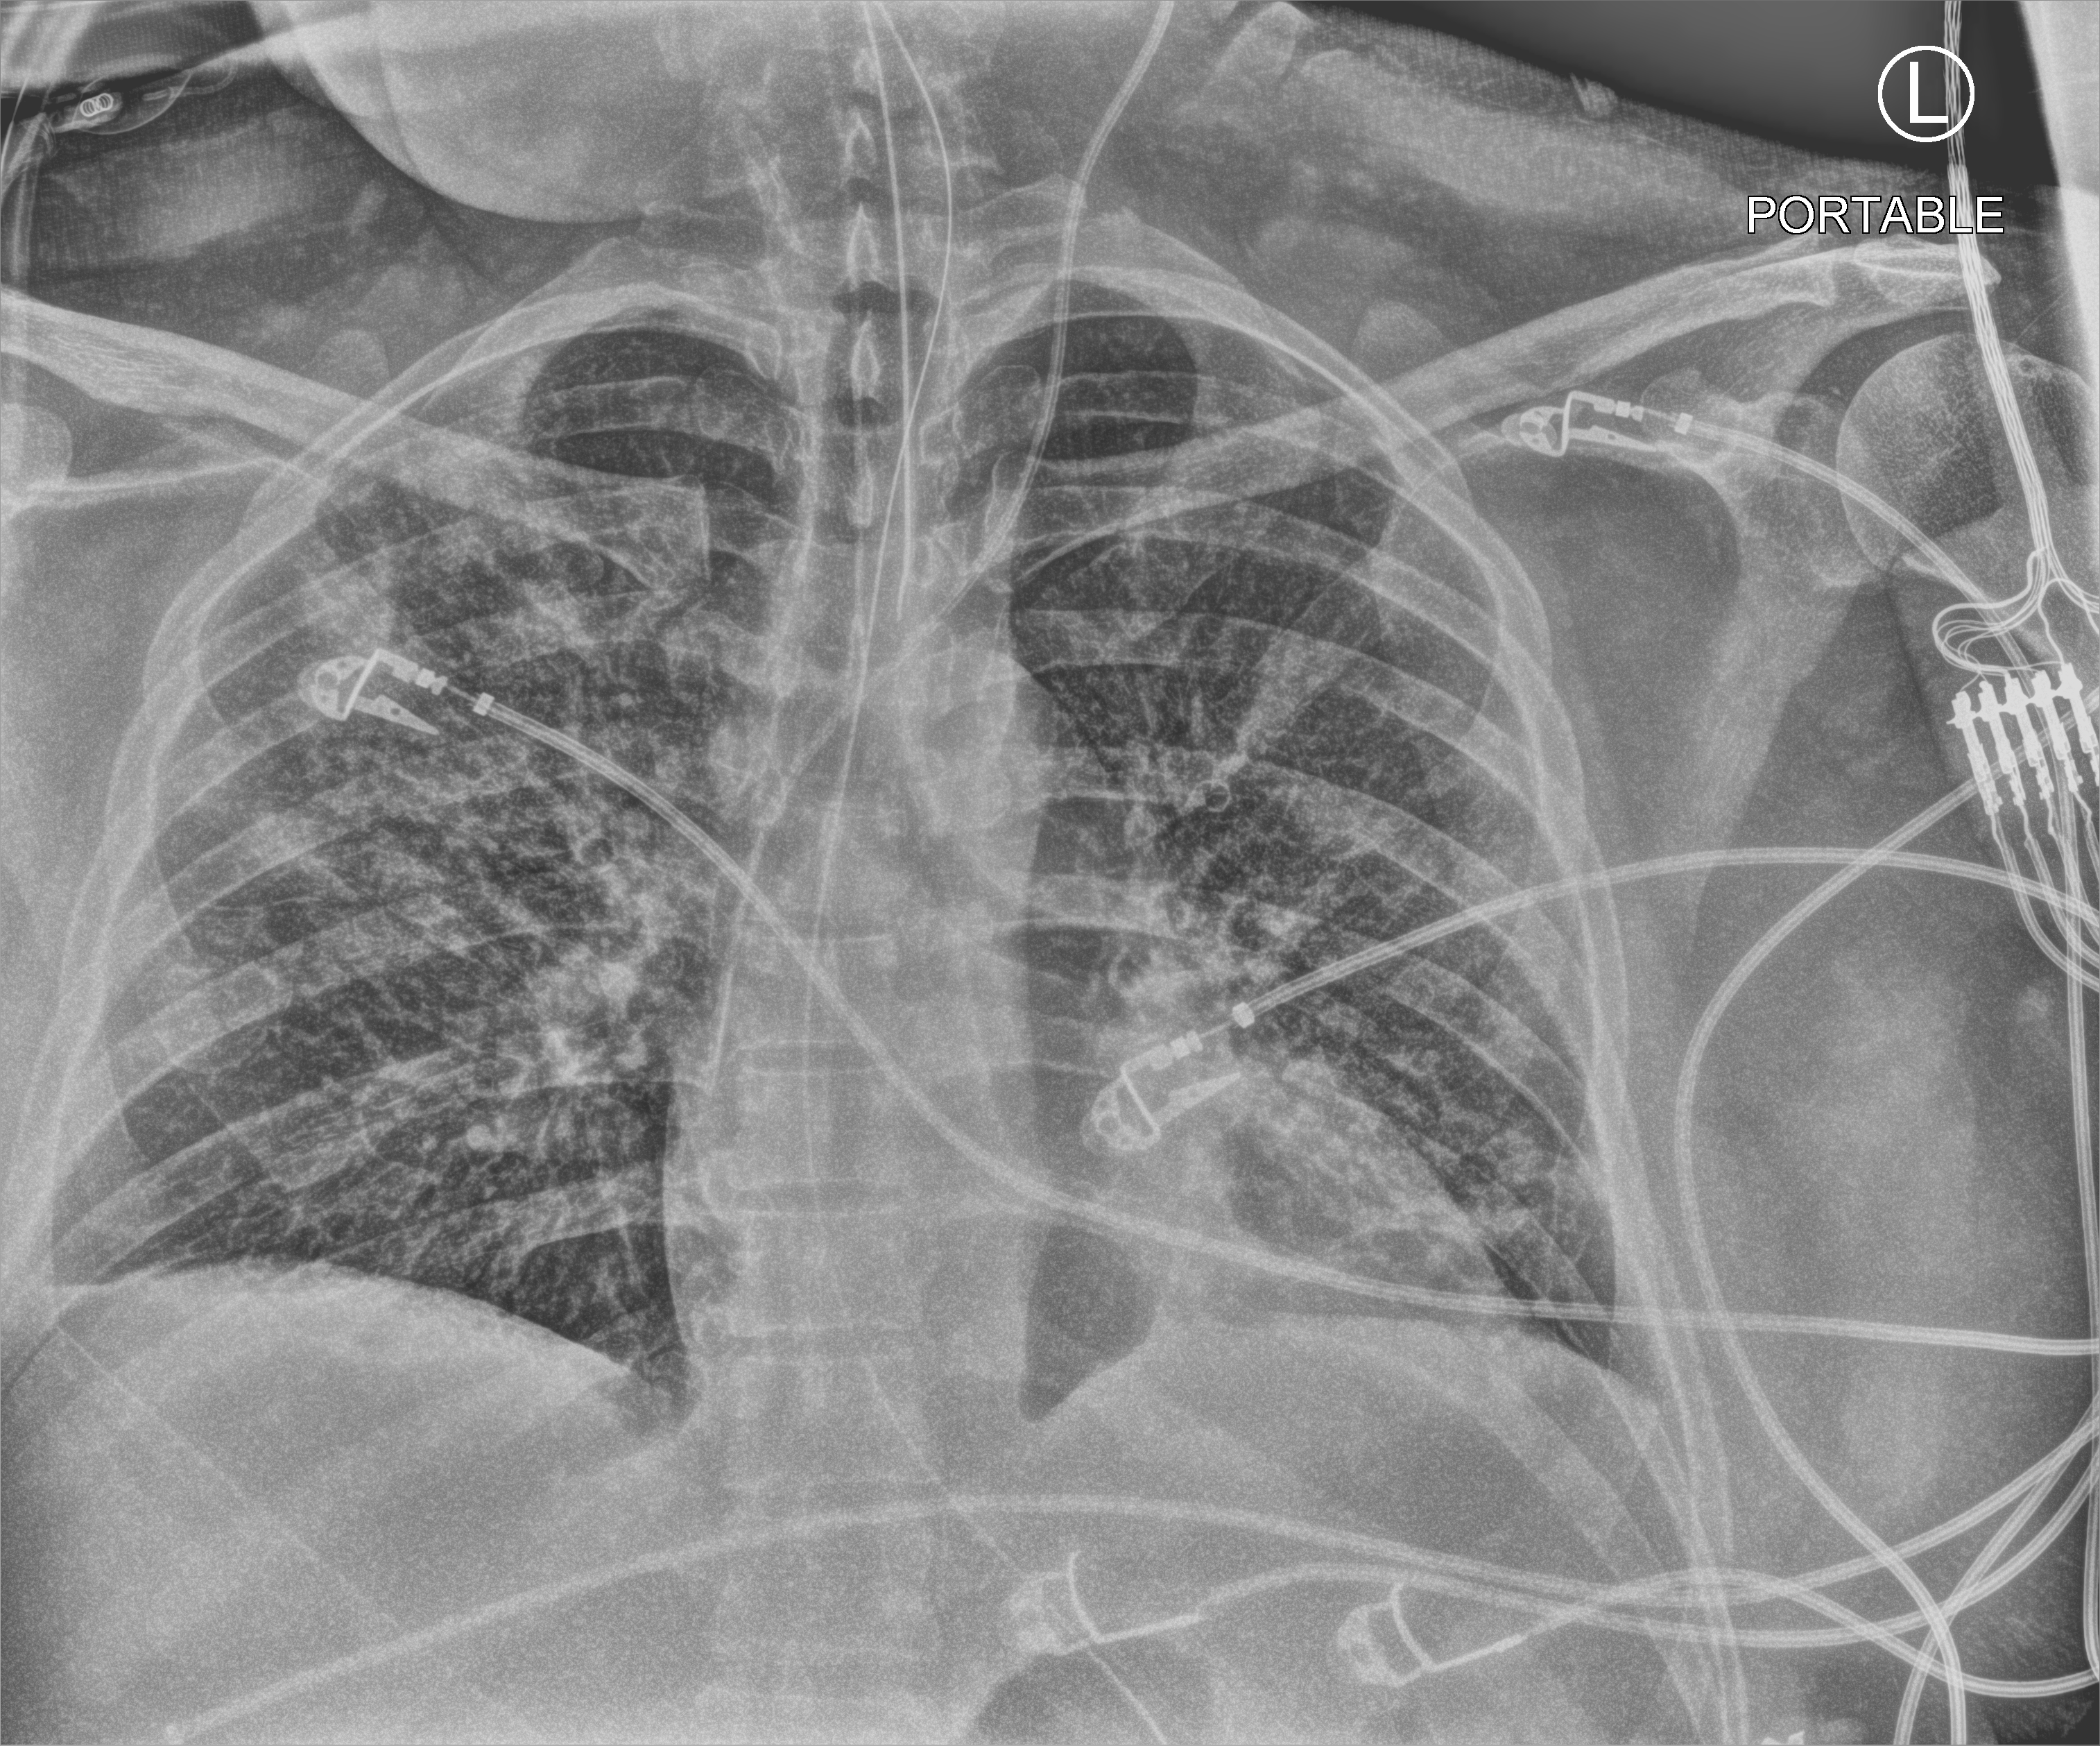
Bedside chest radiograph (computed radiography); anteroposterior (AP) projection. Adult patient hospitalised with COVID-19, age 18–59 years.
Admission-level facts for this patient (not findings on this image; timing relative to this image not recorded): admitted to intensive care during this hospital stay: yes; diabetes (admission record): no; mechanically ventilated during this hospital stay: yes.